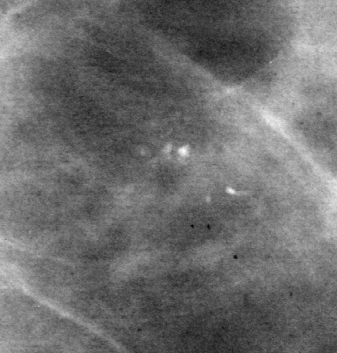
Region of interest cut from a scanned film mammogram (one marked finding); left breast; CC view.
- Calcifications, morphology punctate, distribution clustered; BI-RADS assessment category 4; pathology result (as recorded, not read from the image): benign.